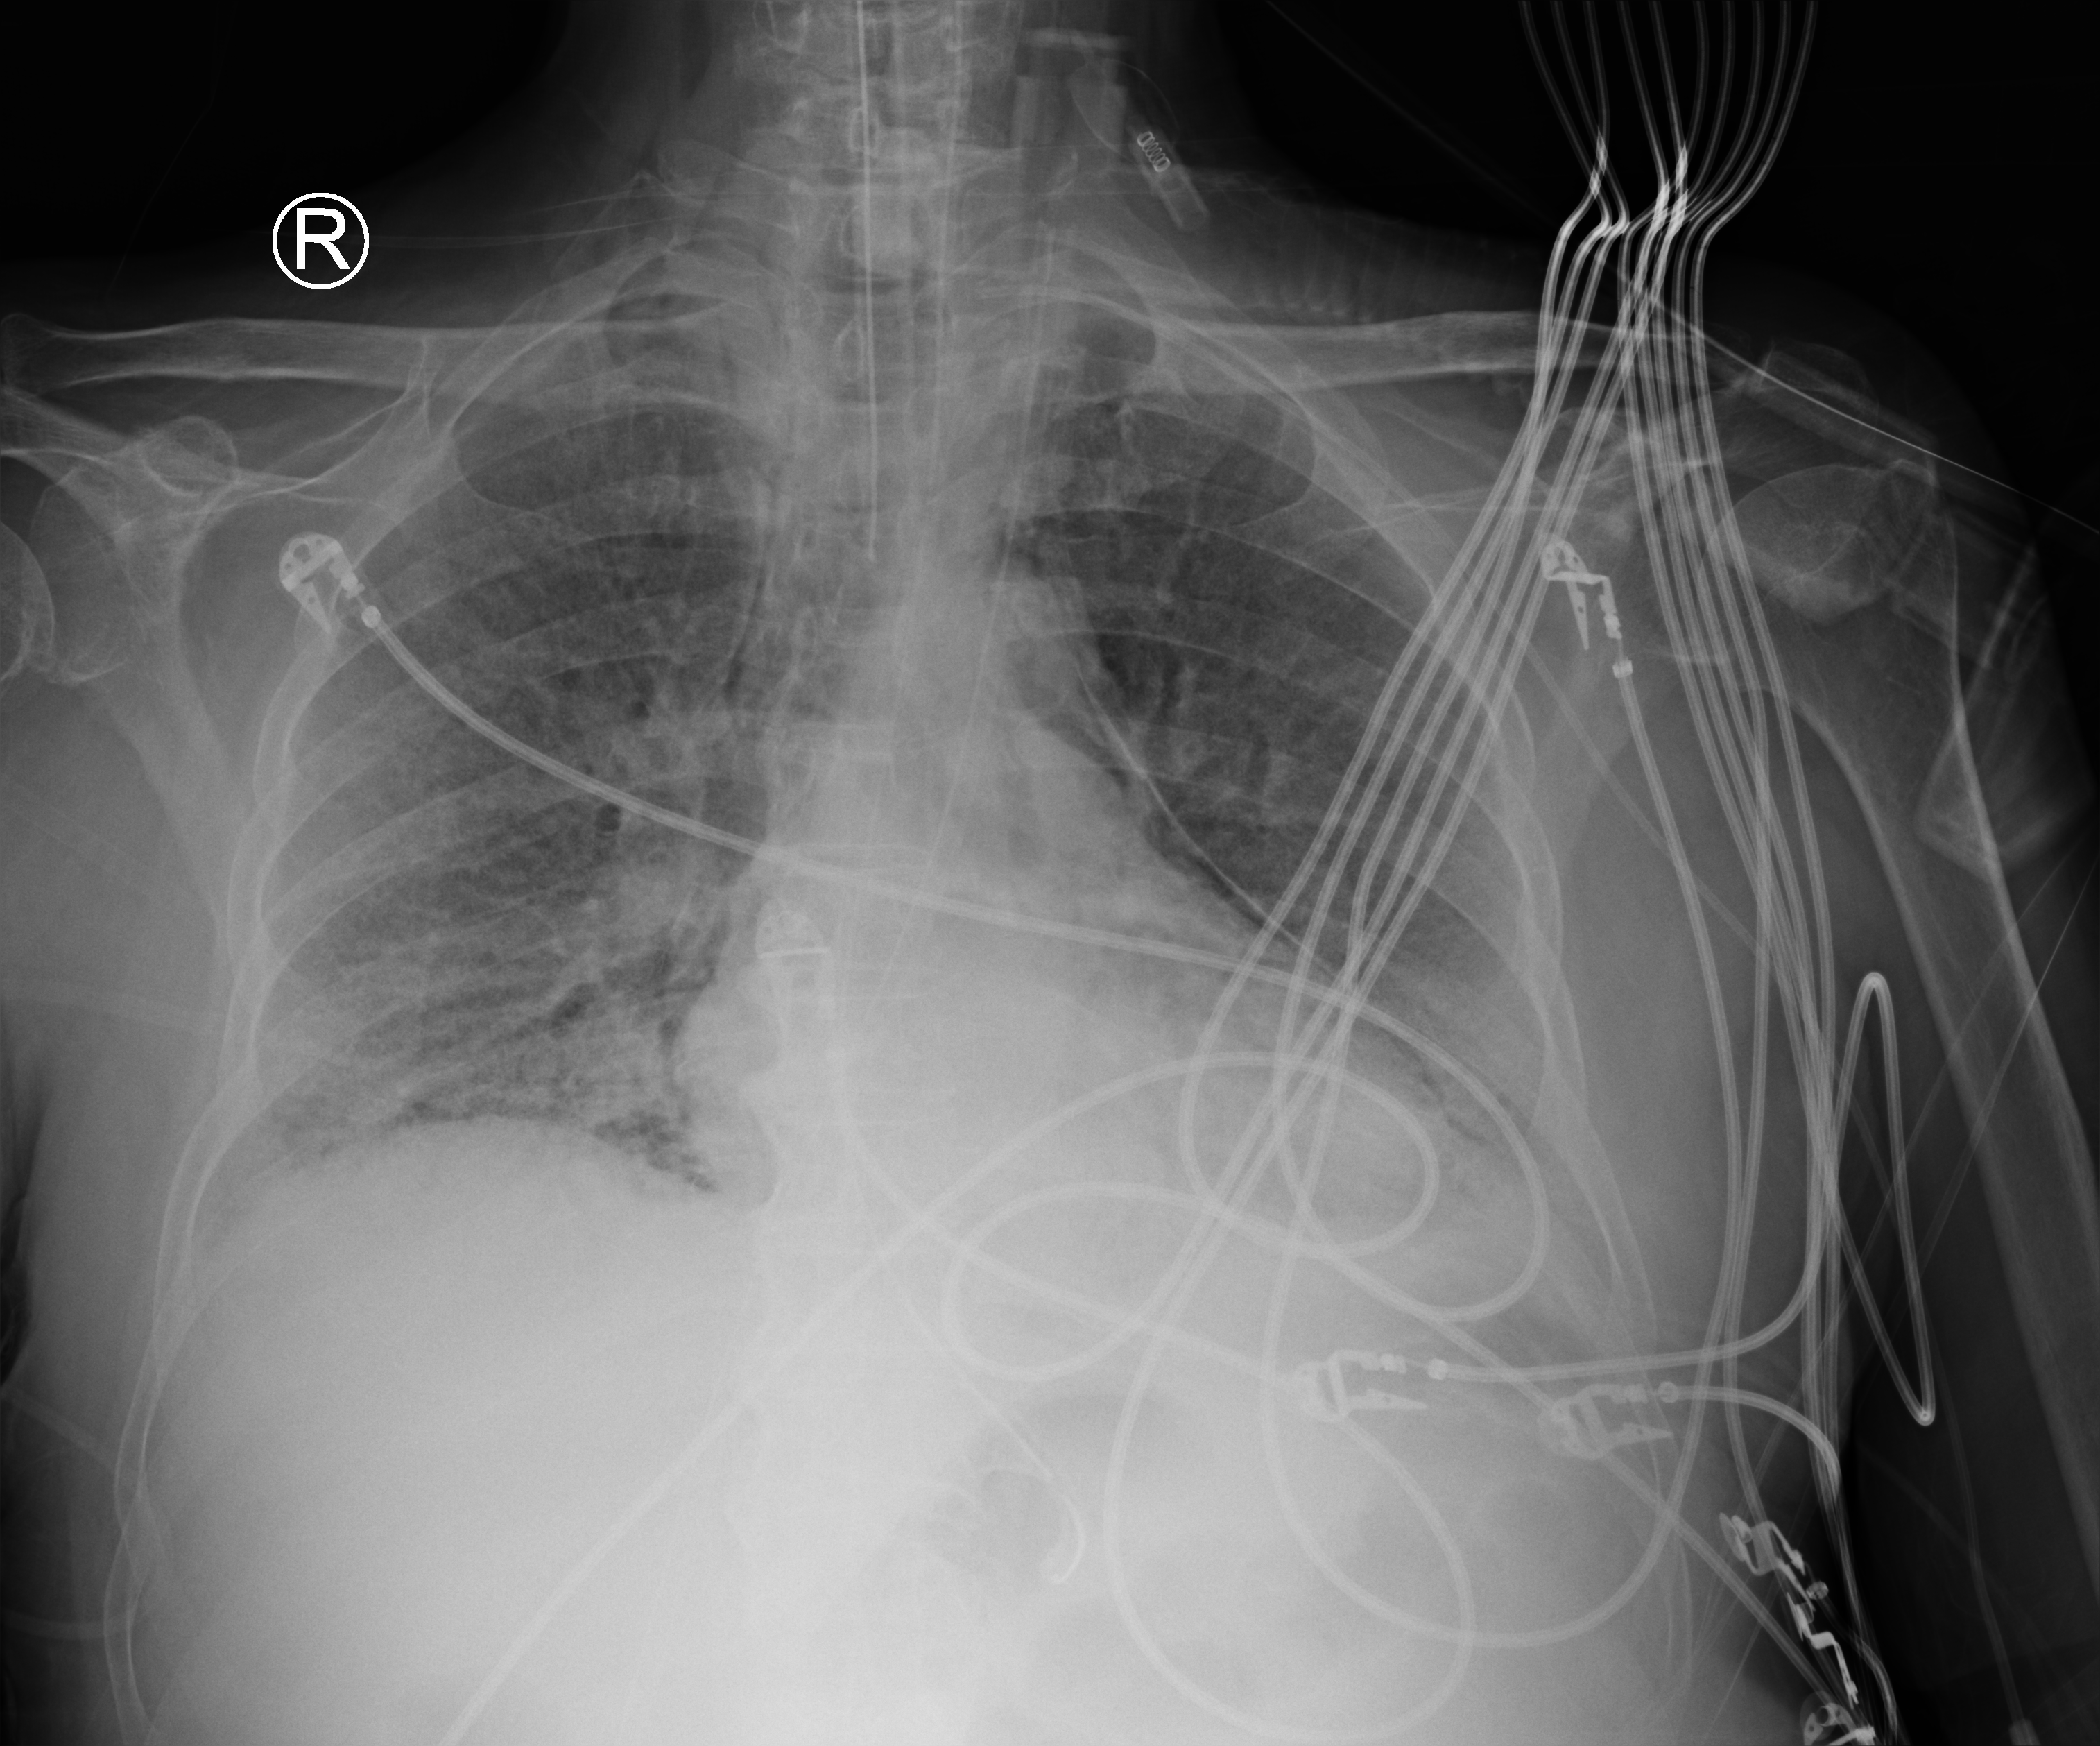
Chest X-ray (portable); anteroposterior (AP) projection. Patient hospitalised with COVID-19; male, aged 75–90 years.
Admission-level facts for this patient (not findings on this image; timing relative to this image not recorded): admitted to intensive care during this hospital stay: yes; COPD (admission record): no; diabetes (admission record): no.